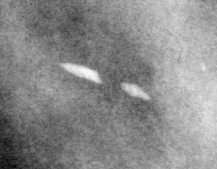
Cropped region of a digitized screen-film mammogram centred on a radiologist-marked abnormality, left breast, CC view.
Finding: calcifications, morphology vascular / coarse; BI-RADS assessment category 2; benign without callback (not worked up further).